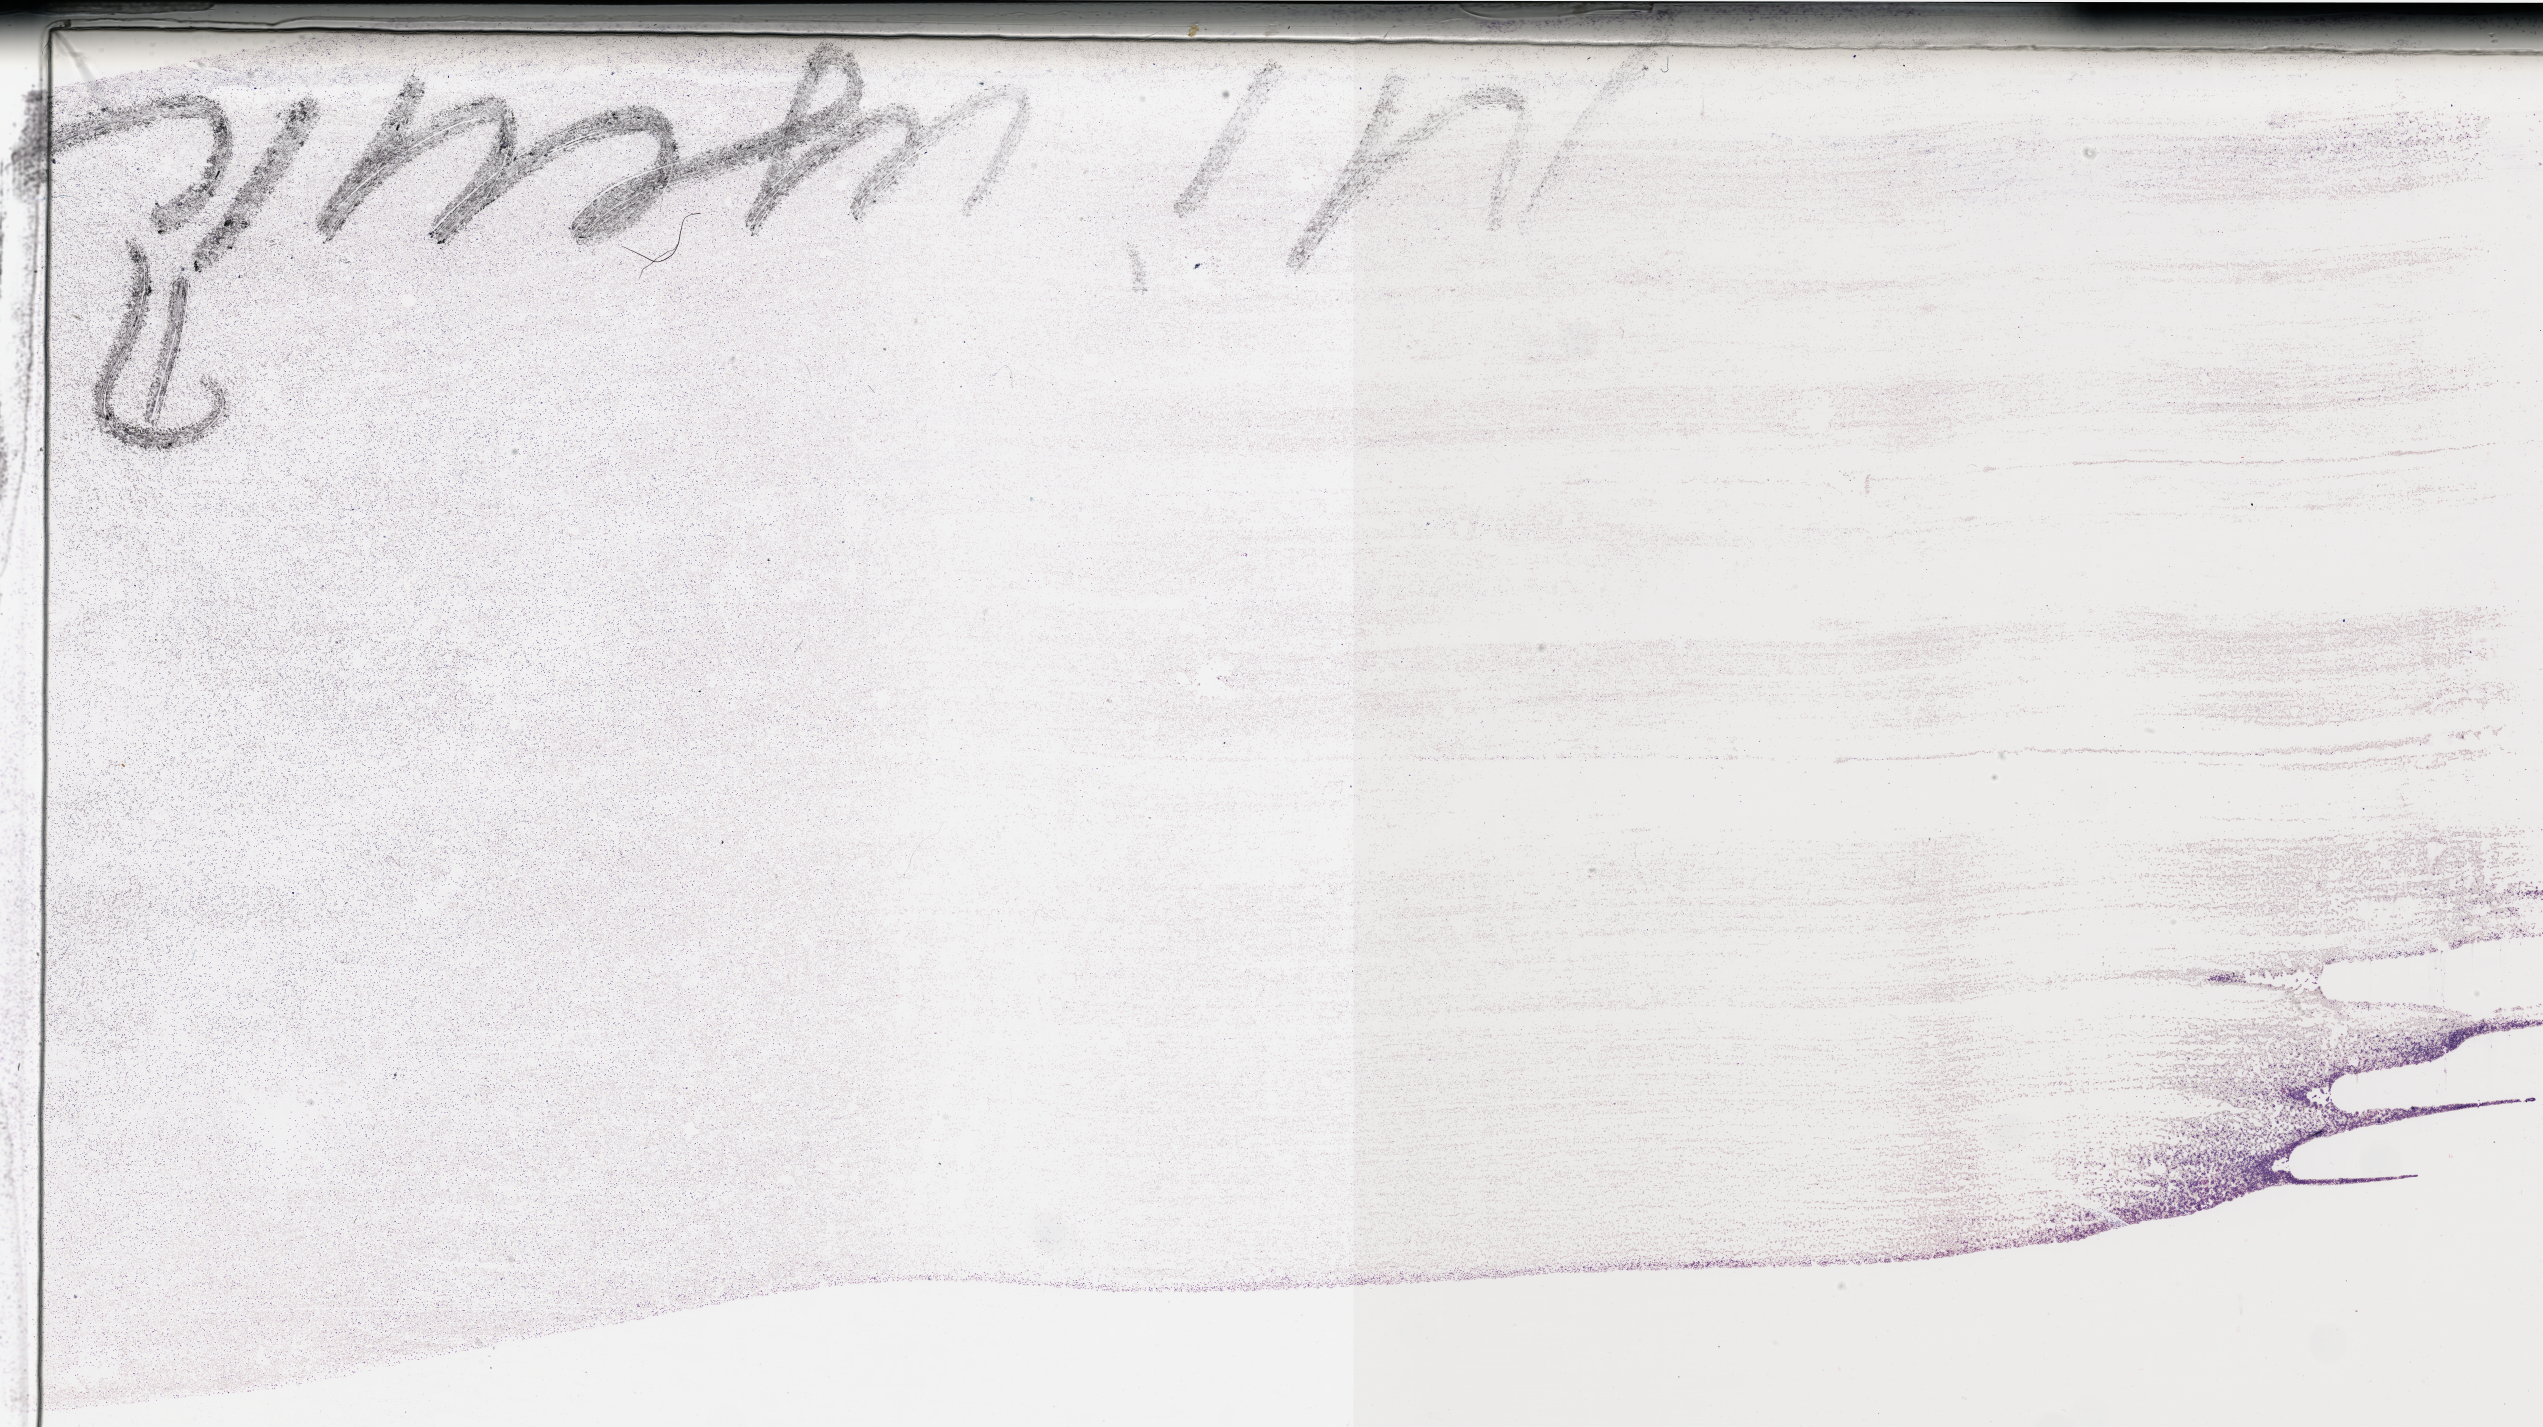
Whole-slide histology image, H&E-stained — a low-resolution overview of the entire scanned area, about 40.2 x 22.5 mm (from a 40x scan); peripheral blood (leukaemic) sample. Patient: male, age 45 years. Blasts: 25%.
* FAB classification: M4
* diagnosis: Acute Myeloid Leukemia